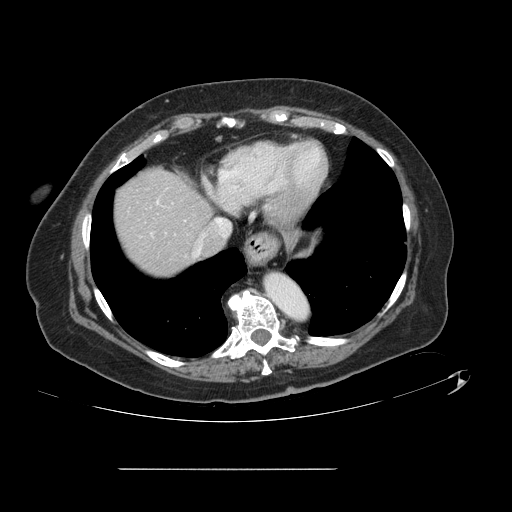
Contrast-enhanced abdominal CT, one axial slice; intravenous contrast given; soft-tissue window (W 400 / L 40 HU); 512 × 512 image matrix, field of view 439 × 439 mm. Female patient, age 75 years. From the clinical record (not read from this slice): diagnosis: colorectal cancer liver metastases, imaged before liver resection; multiple liver metastases: no; largest metastasis: 2.4 cm; disease in both lobes: no.
Annotated regions visible in this slice (manually delineated by an expert):
- hepatic veins: bounding box <195,218,230,256> (left, top, right, bottom; pixels)
- liver: <114,169,210,277>
- planned liver remnant (the part of the liver to remain after resection): <114,169,210,277>